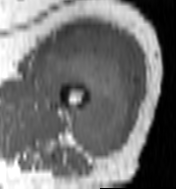
MRI of an extremity soft-tissue mass, one axial slice; slice 71 of 100 in the series (ordered by position); MR volume resampled by the dataset authors to the PET/CT grid (not the native acquisition matrix); 3.27 mm slice thickness; 176 × 189 image matrix, field of view 172 × 185 mm. Female patient. From the clinical record (not read from this slice): histological type: undifferentiated – high grade; grade: high; site of the primary tumour: left thigh.
Structures marked on this image (expert contour drawn on MRI and transferred to this co-registered scan by the dataset authors):
- gross tumour volume including surrounding oedema: bounding box (x1, y1, x2, y2) in pixels: (44, 34, 136, 158)
- gross tumour volume (mass): (44, 34, 136, 158)